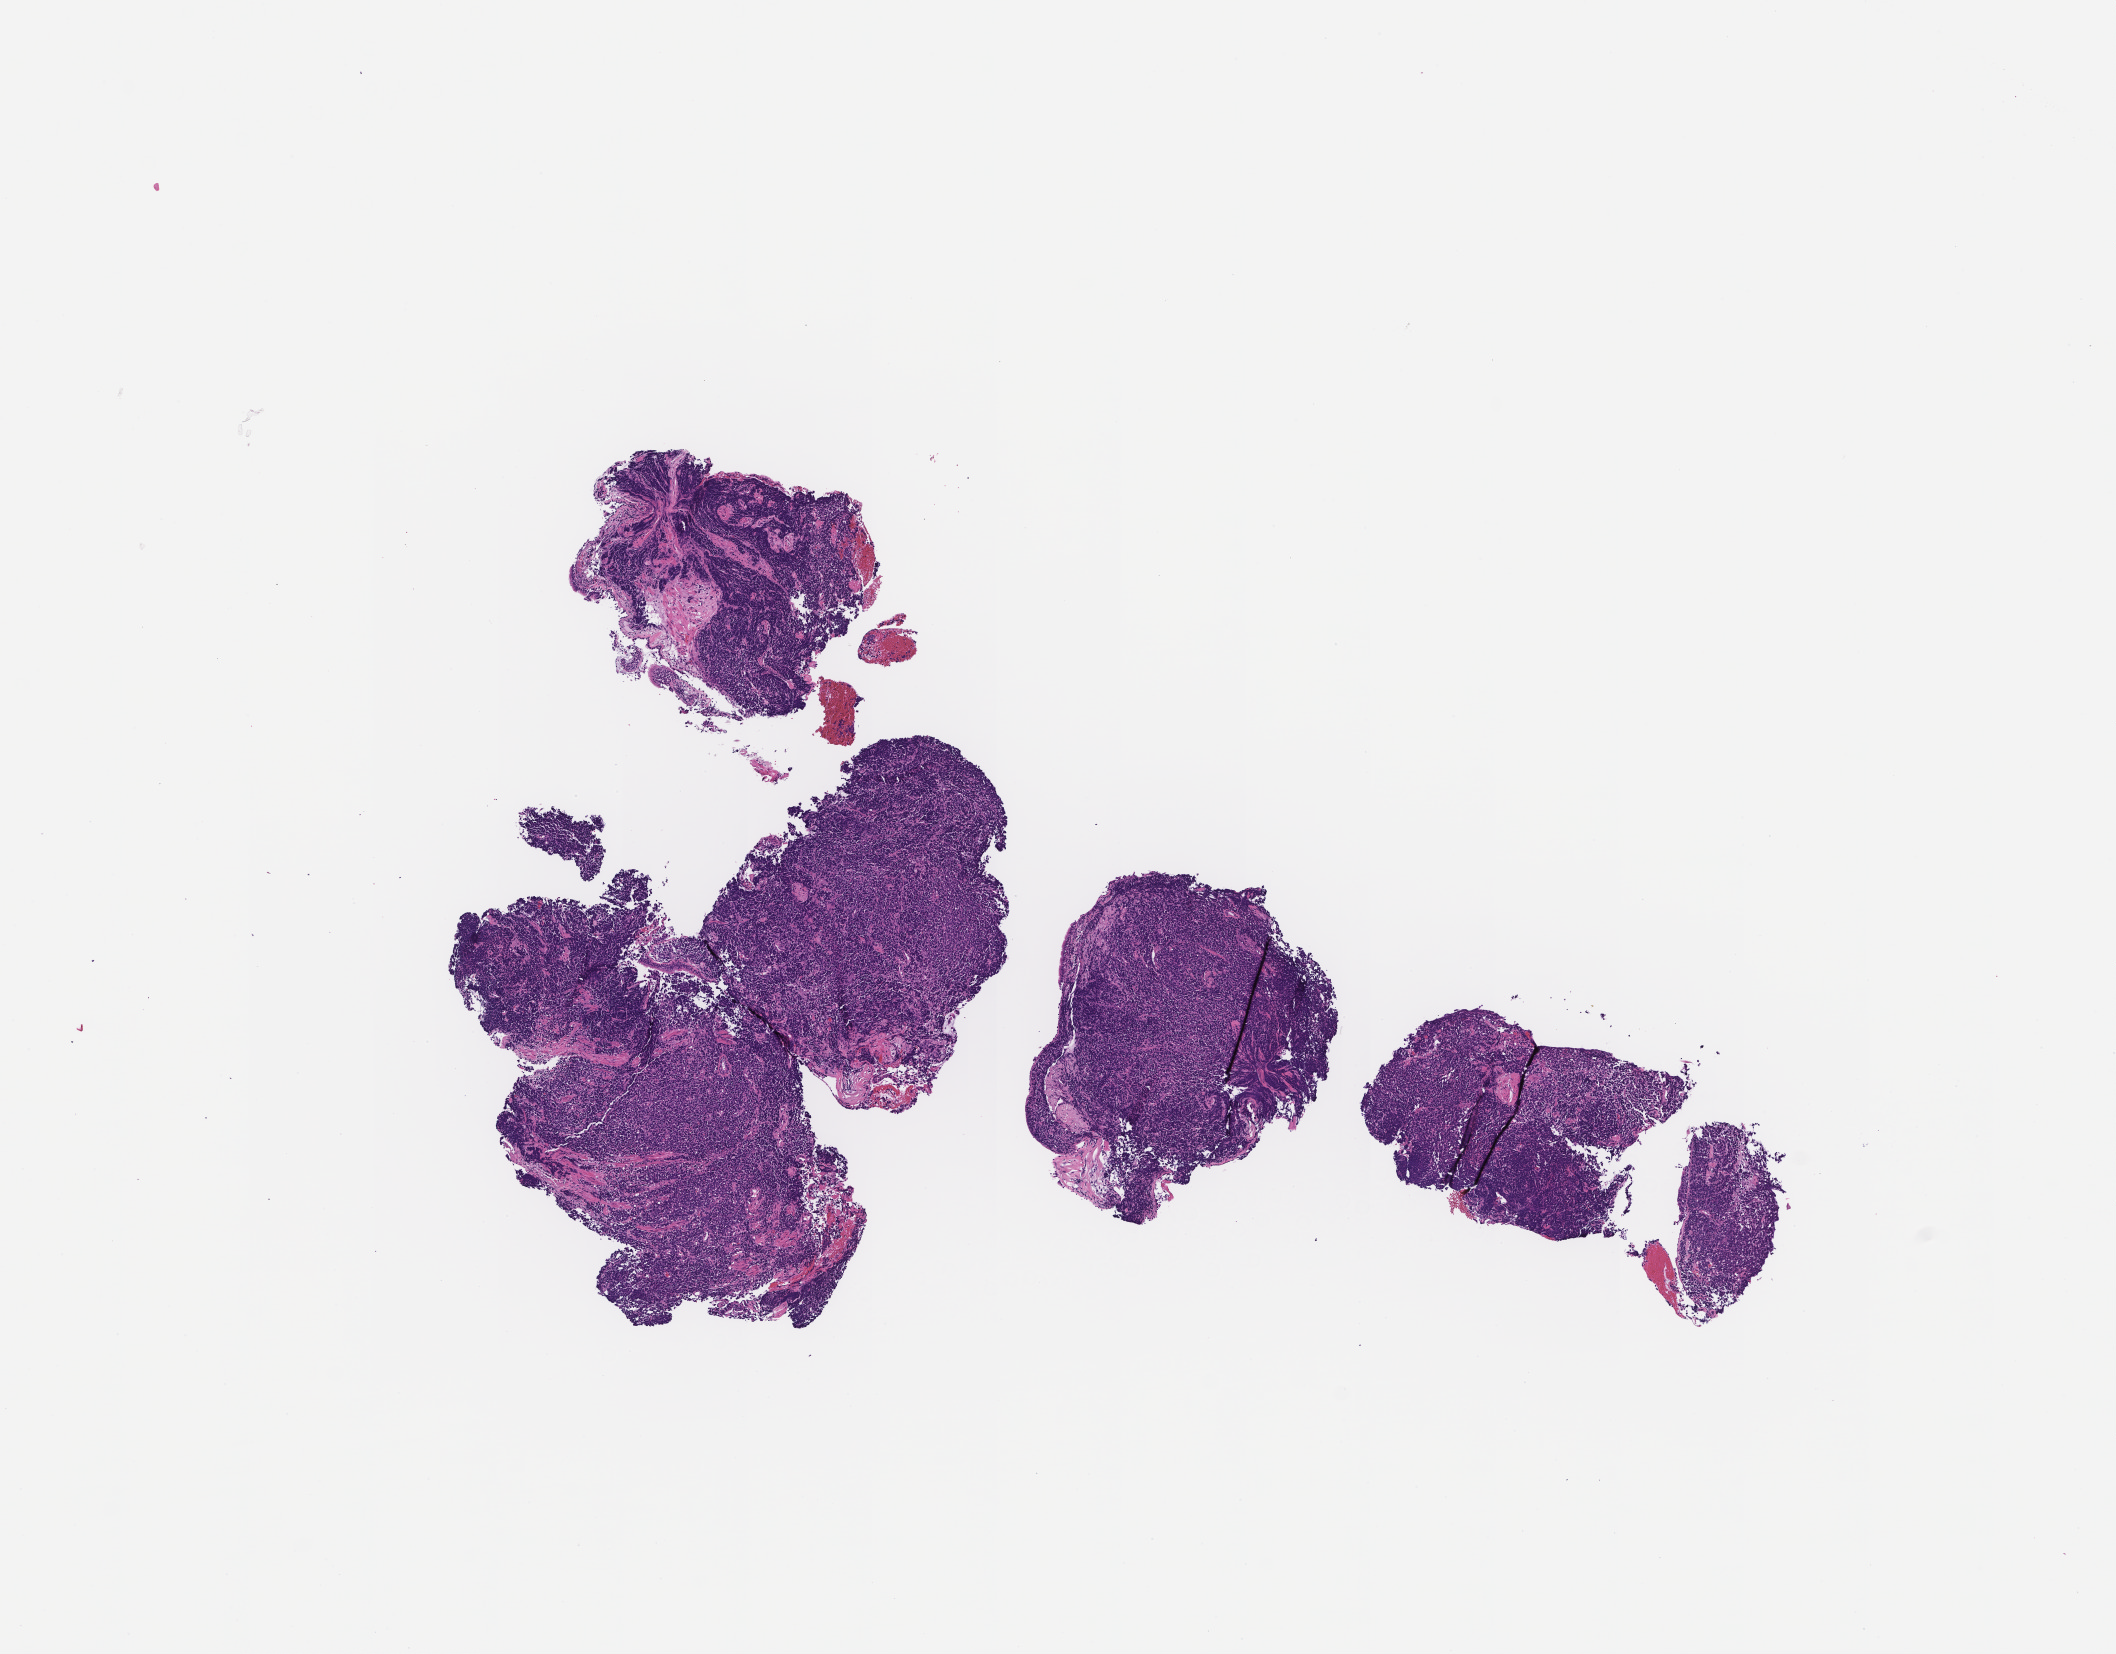
Hematoxylin and eosin (H&E) whole-slide image, low-resolution overview of the scanned area, about 8.5 x 6.7 mm, FFPE section, tissue site: lung. Patient sex: female.
This section: primary tumor. Diagnosis: Small Cell Lung Carcinoma.